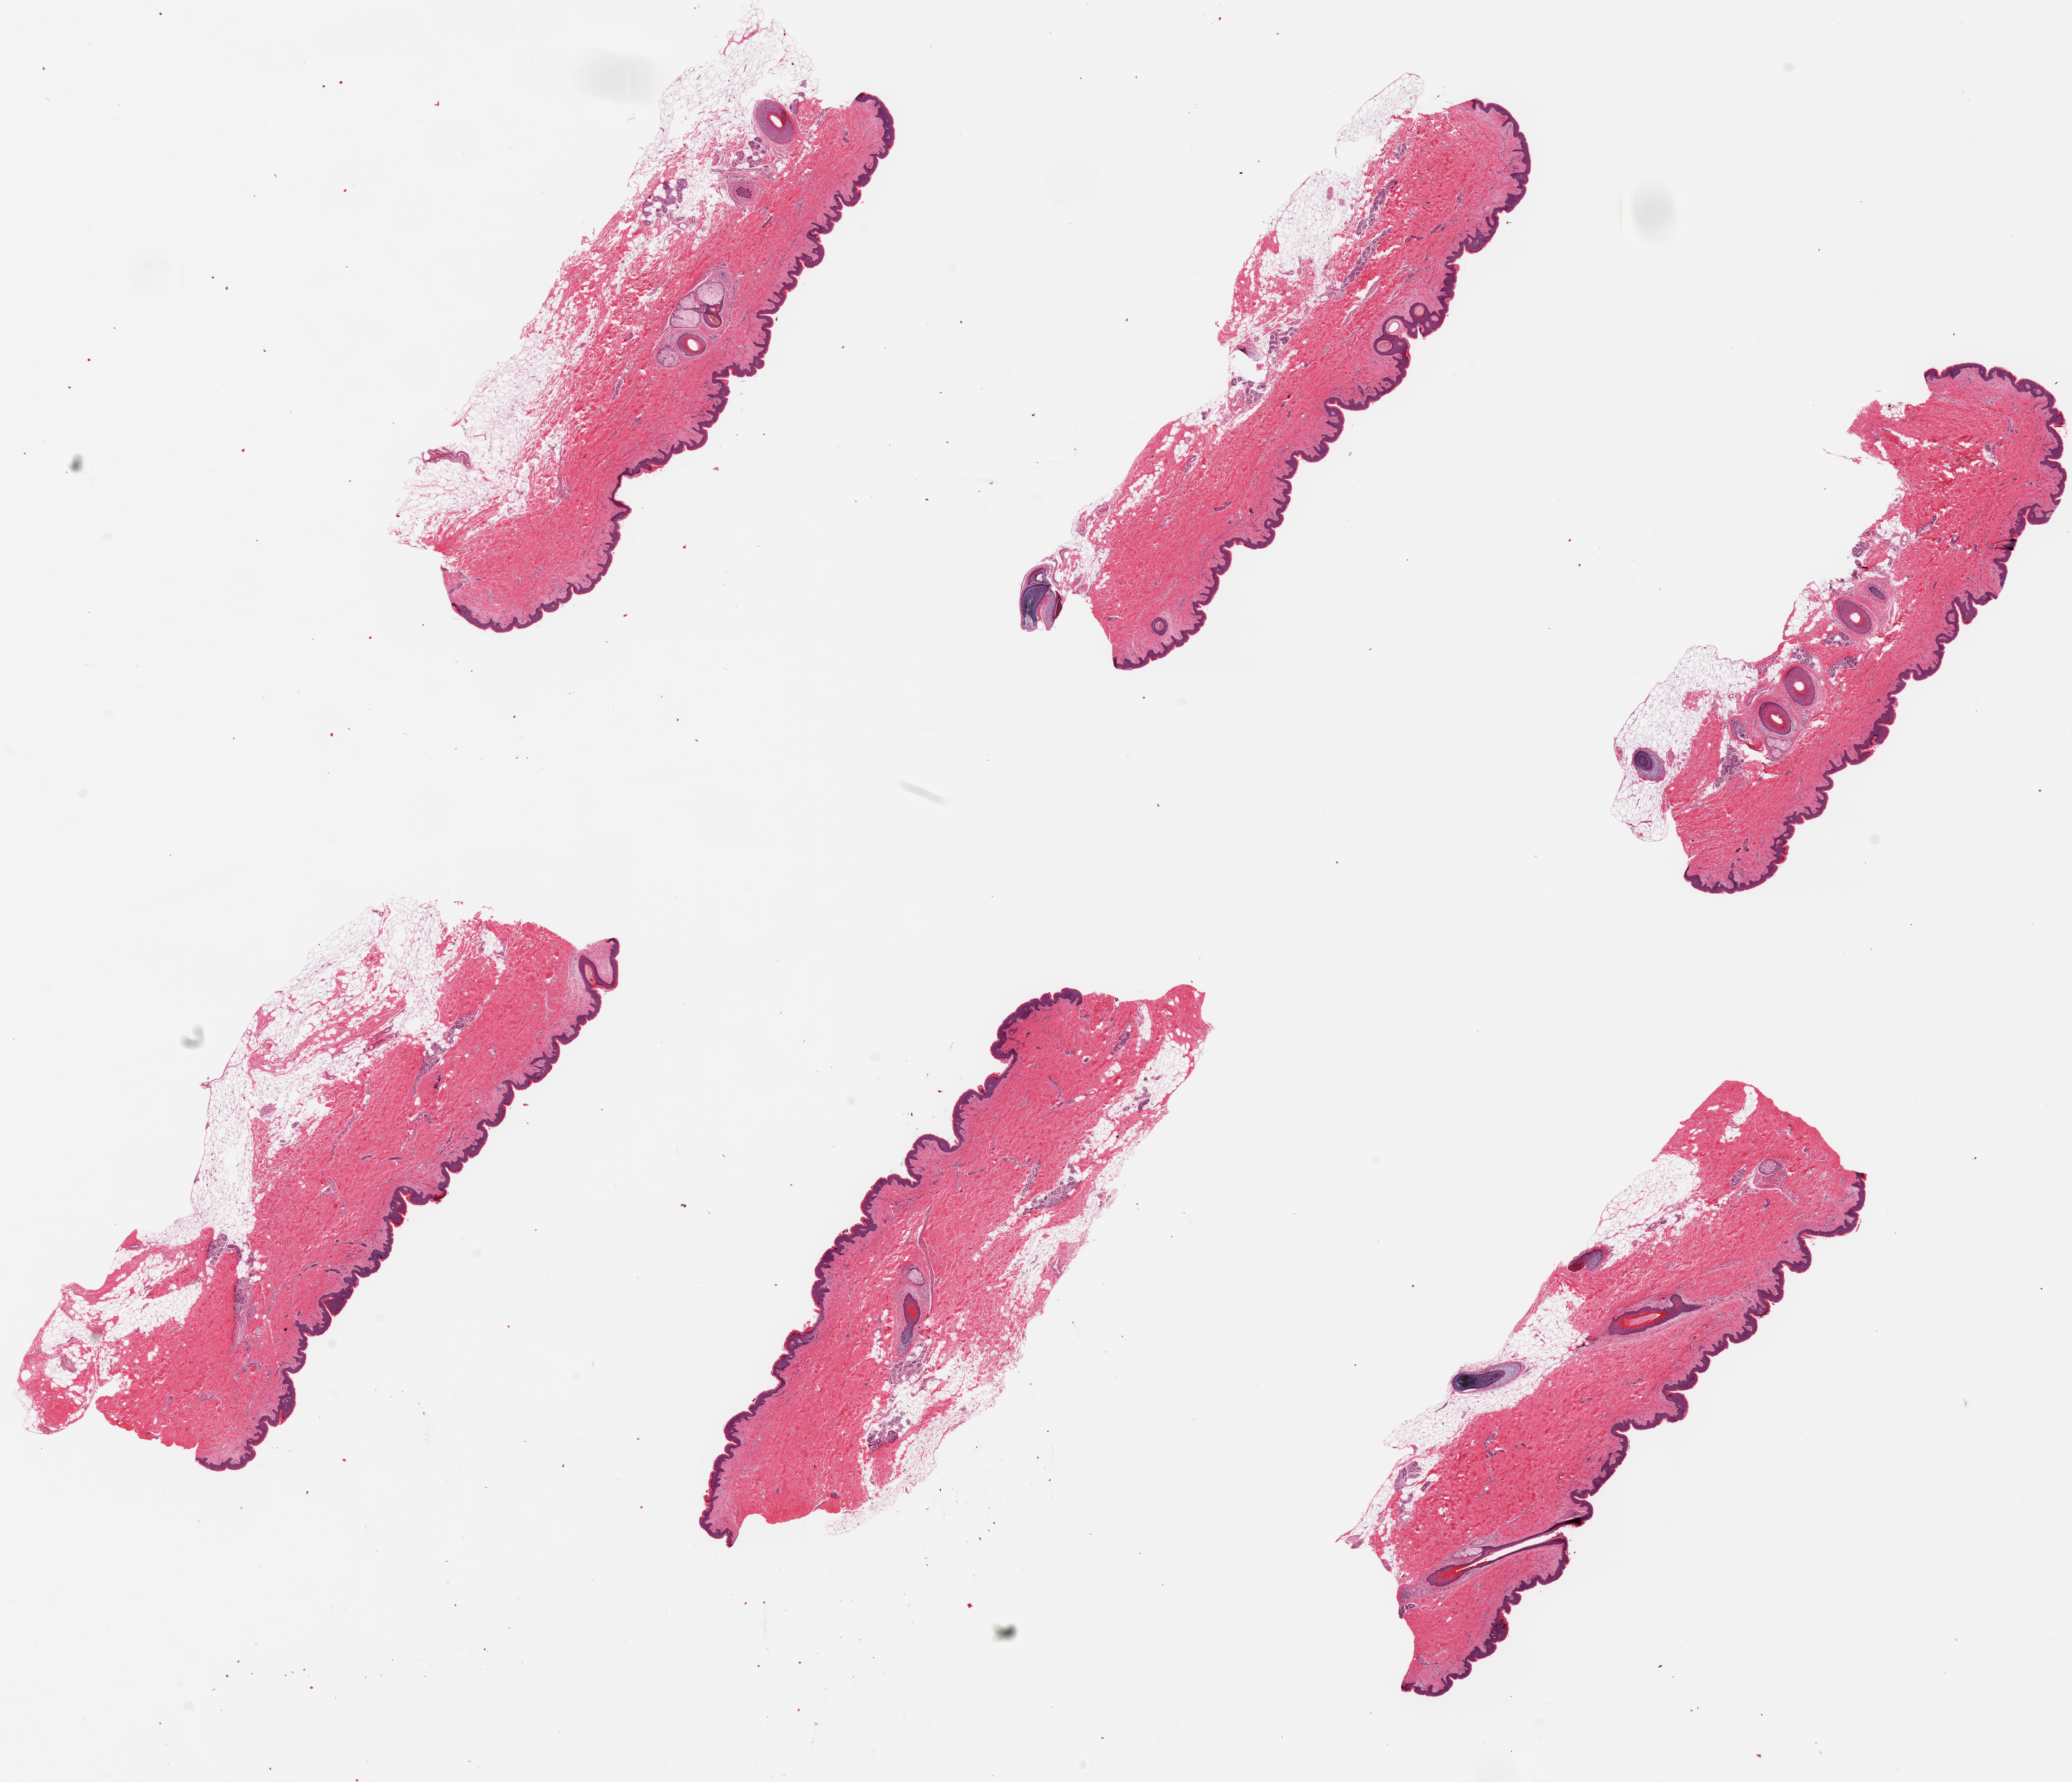
Whole-slide image, hematoxylin and eosin (H&E) stain — shown as a low-resolution overview of the whole scanned area (about 22.6 x 19.5 mm, from a 20x scan); PAXgene-fixed, paraffin-embedded tissue; target tissue: skin of suprapubic region; tissue donor sample. Male donor.
- reviewer comment on this tissue sample: 6 pieces, up to 8x2mm; squamous epithelium is ~3-5% of thickness